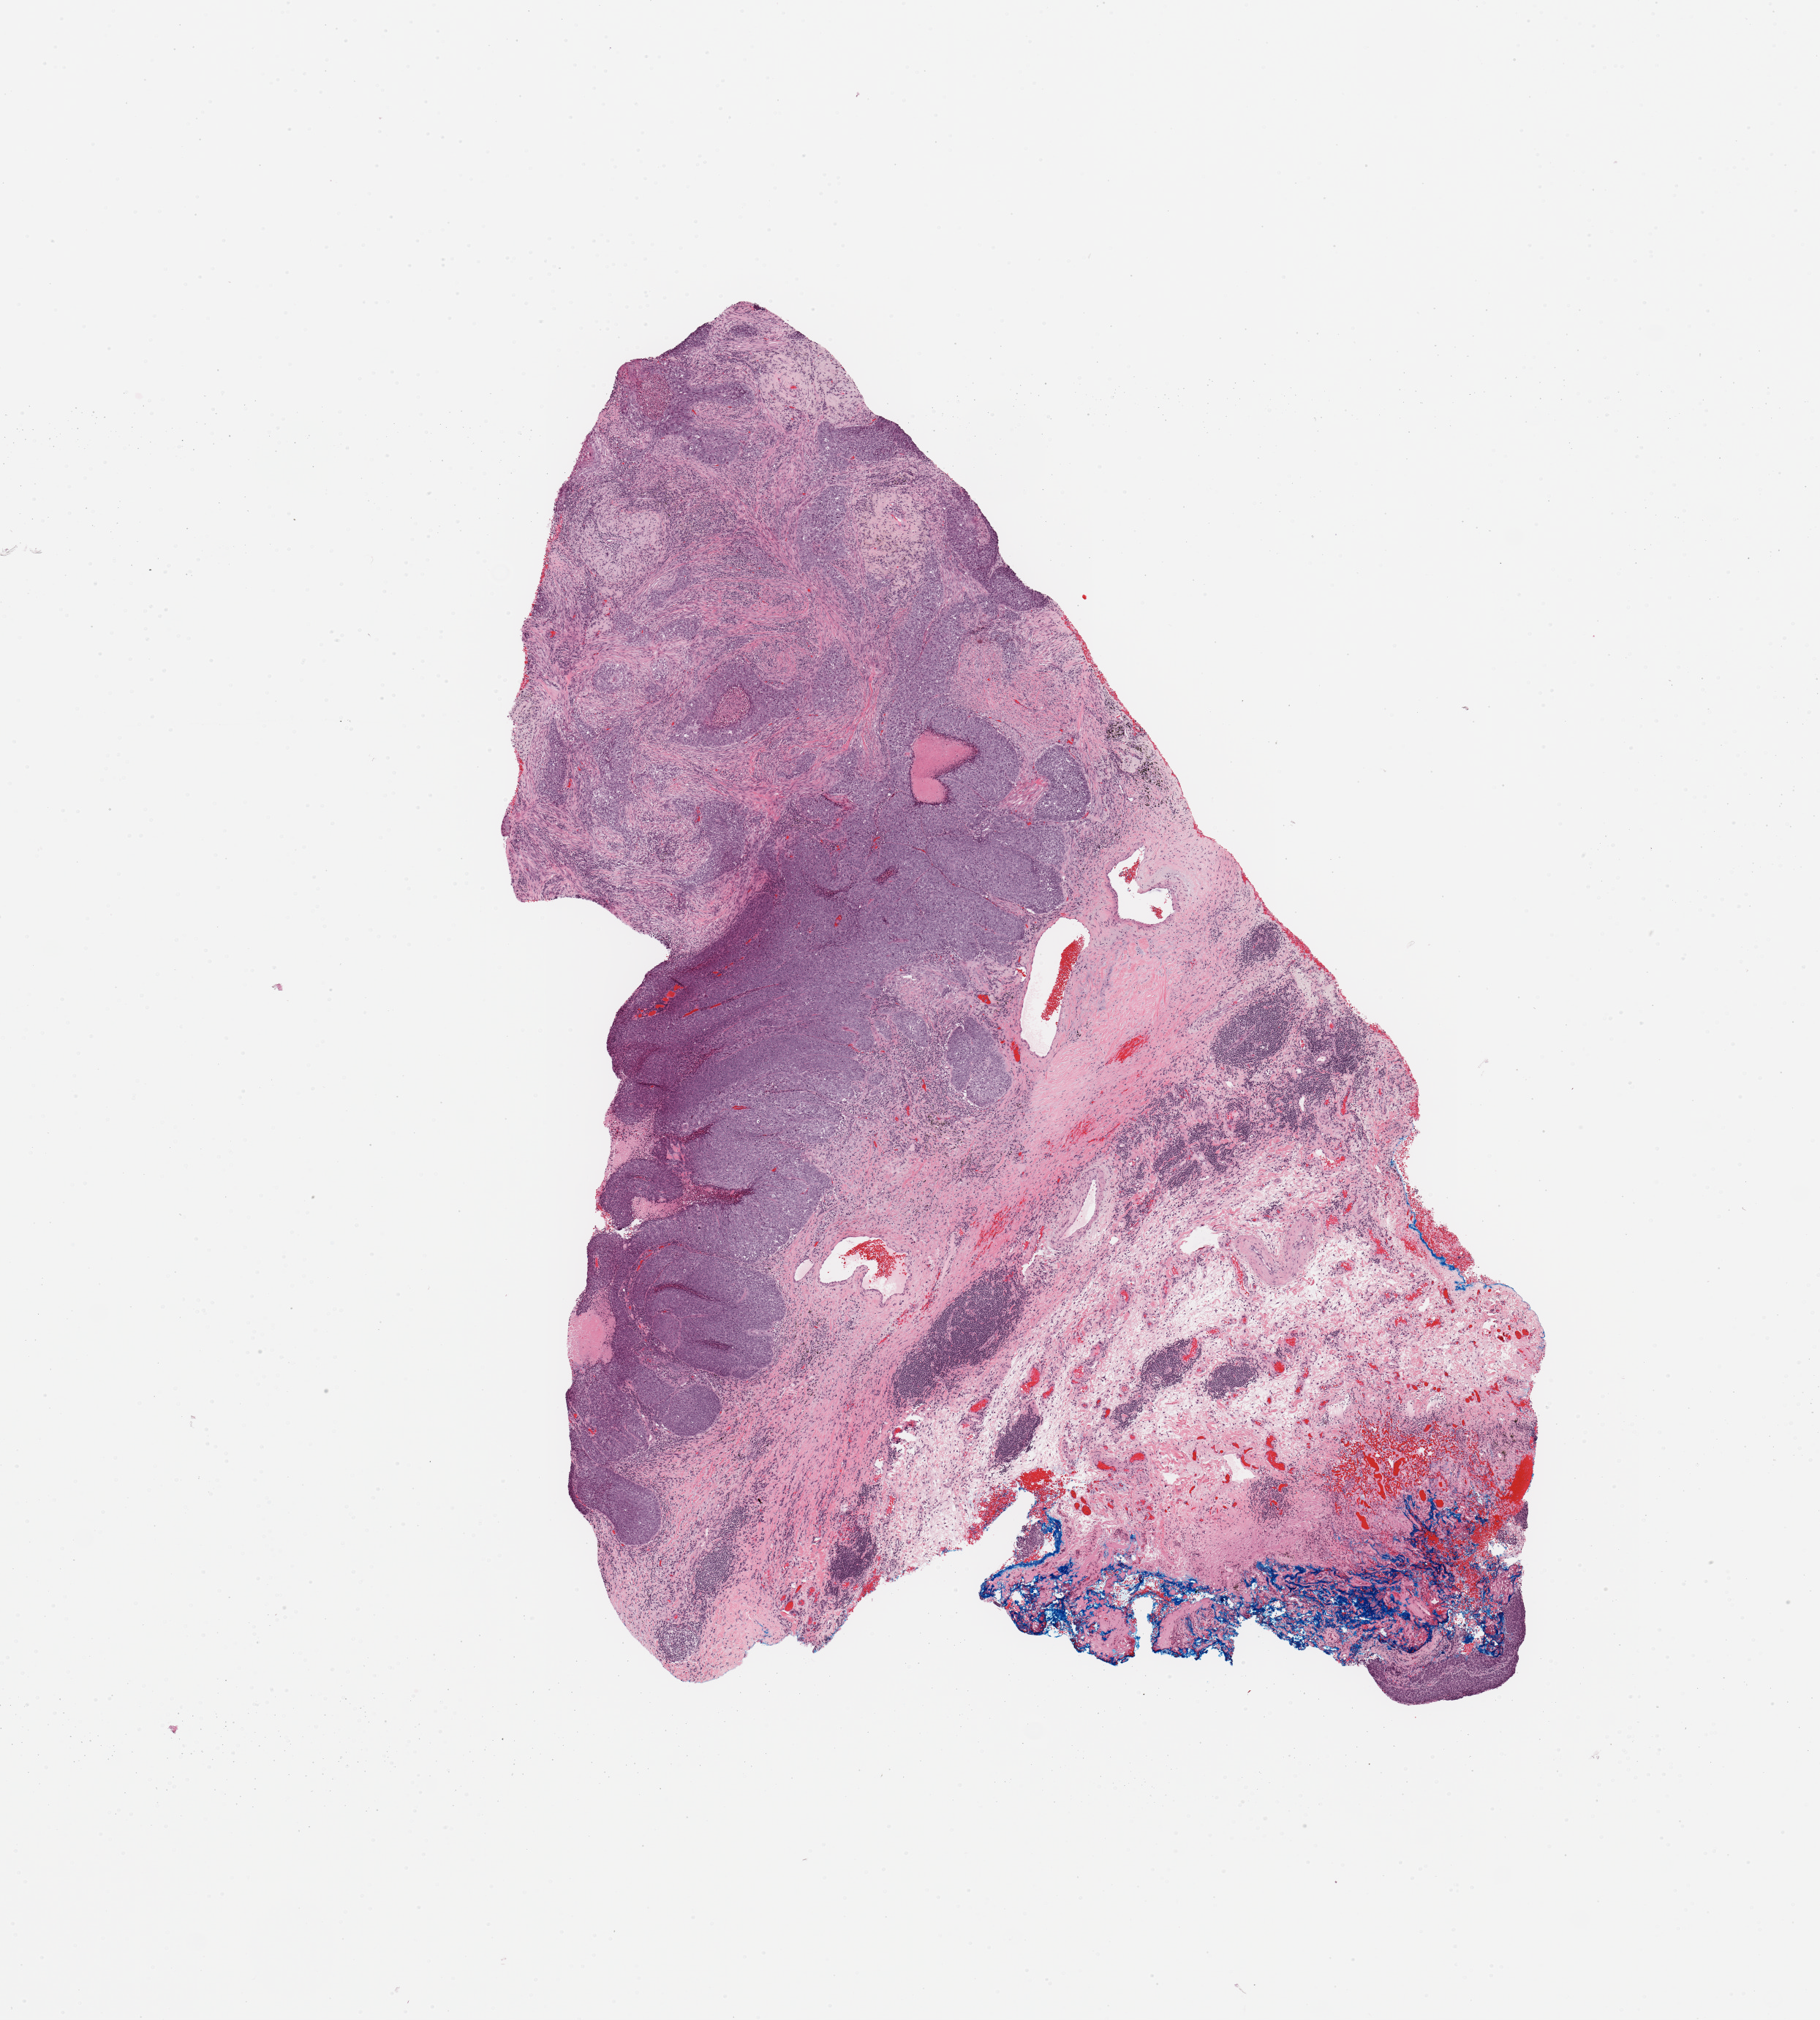
Digitized H&E tissue section (whole slide), a low-resolution overview of the entire scanned area, about 9.8 x 10.9 mm (from a 20x scan). Tumour tissue sample, sampled site: lung. Patient: male, age 72 years. Histologic grade: G3 (poorly differentiated). Slide review estimates, as recorded: tumour nuclei 60%, necrosis 10%.
• histologic diagnosis: Squamous cell carcinoma, NOS
• AJCC pathologic stage: IA
• primary tumour site (as recorded): right upper lobe